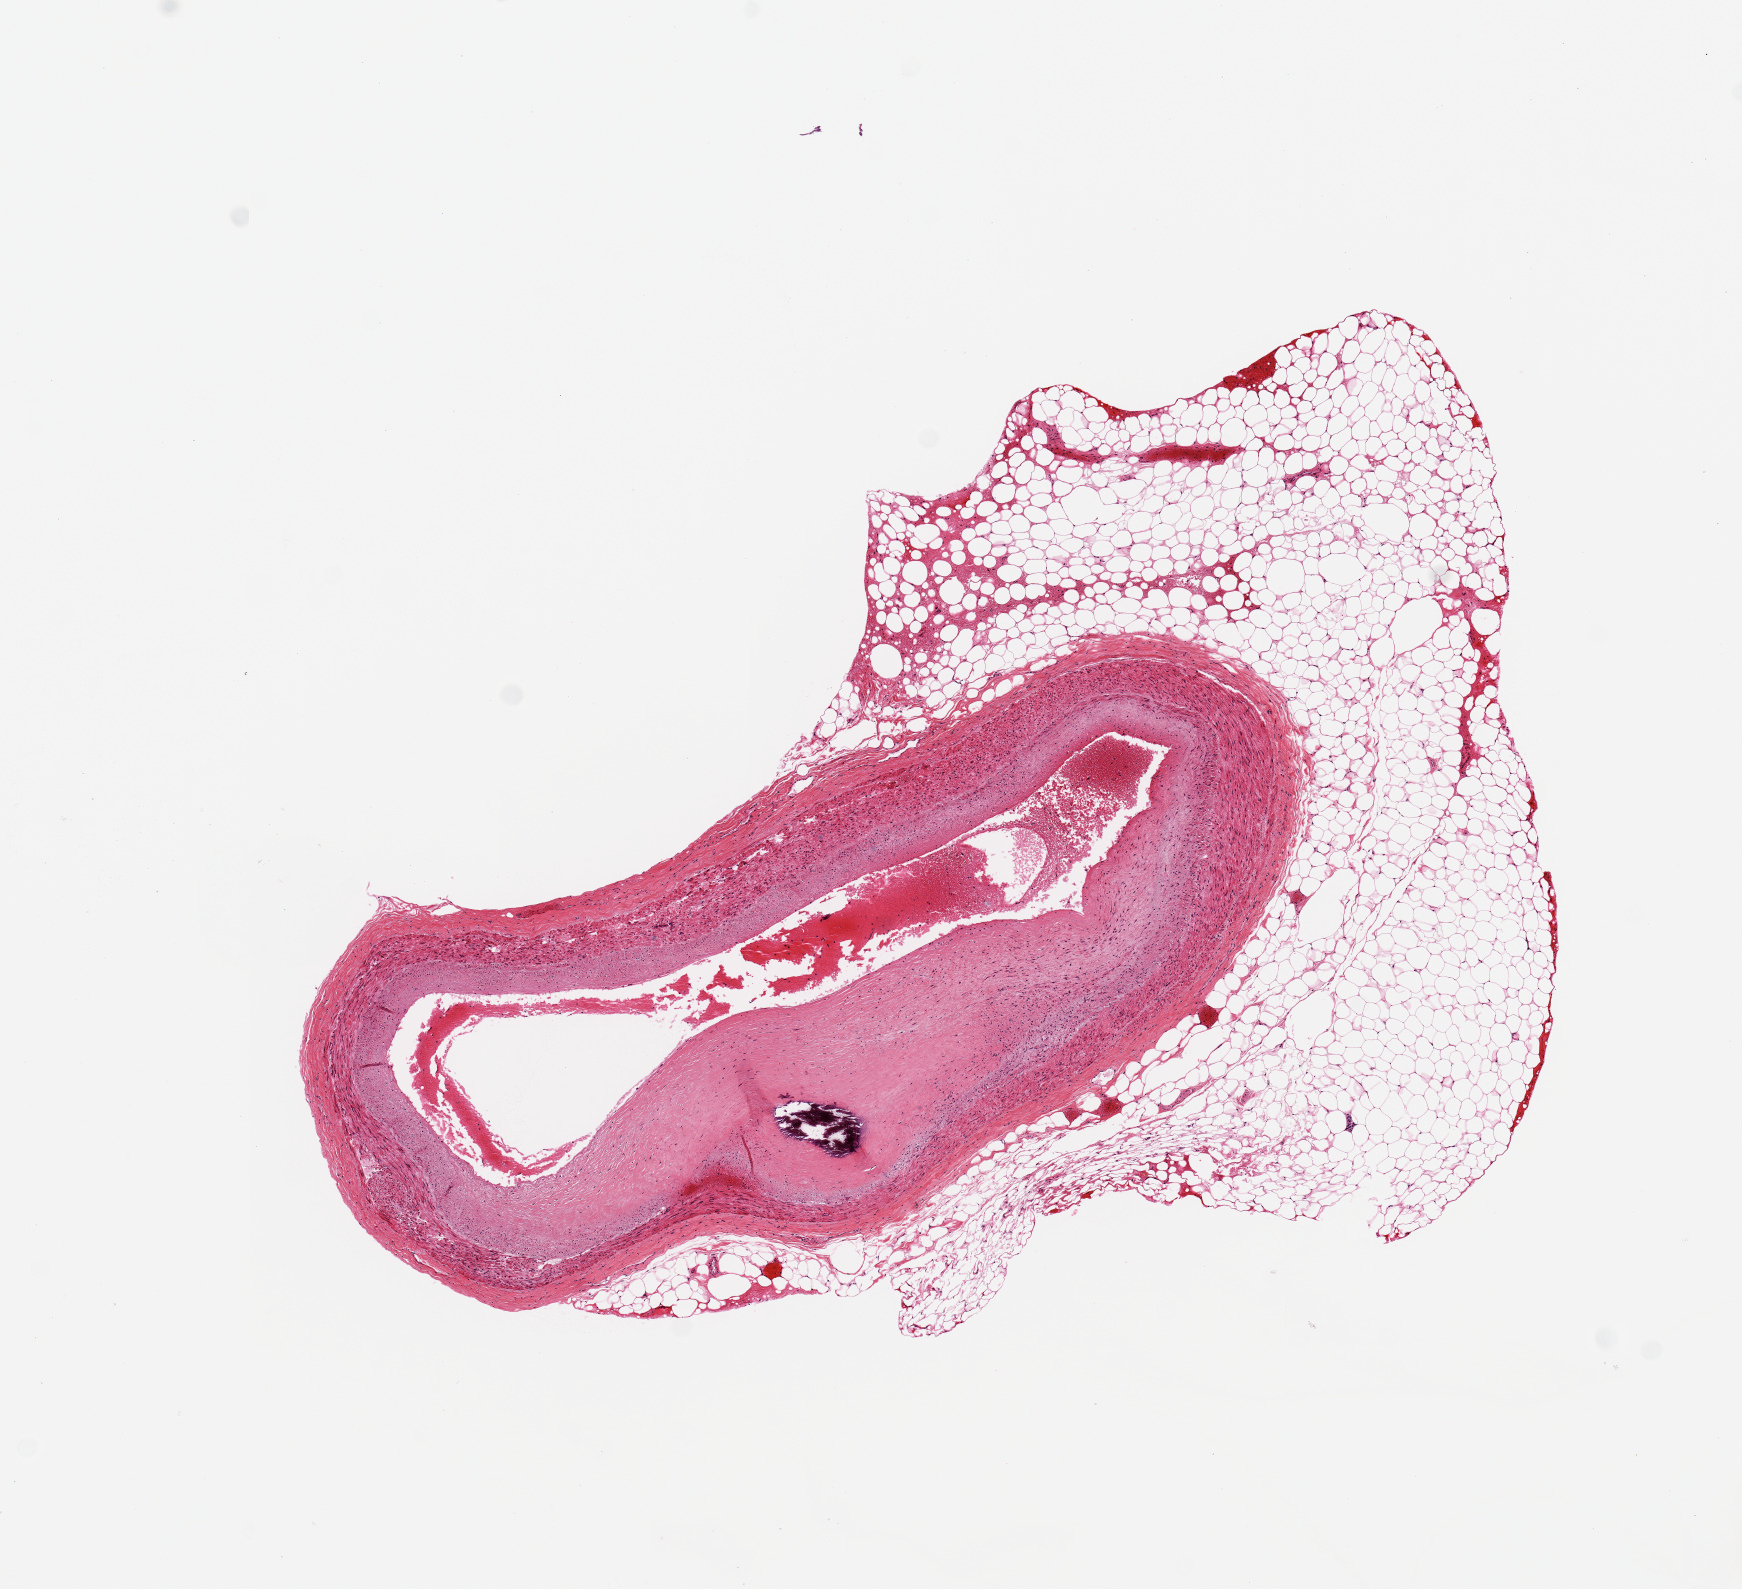
Whole-slide image, H&E stain, low-resolution overview of the scanned area, about 6.9 x 6.3 mm; PAXgene-fixed paraffin-embedded (PFPE) section; section of coronary artery (target tissue); tissue donor sample.
Pathologist's review note for this sample: 4.1x 1.6mm vessel with 60% occlusion by partially calcified atheromatous deposits. 3 x 1mm nodule of fat on one edge.